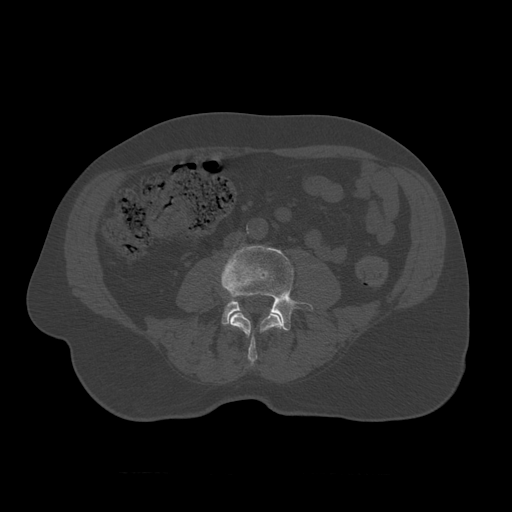
CT including the spine, one axial slice; reconstruction kernel STANDARD; 120 kVp; bone window (W 1800 / L 400 HU); 1.25 mm slice thickness; 512 × 512 image matrix. Patient age 75 years. From the clinical record (not read from this slice): primary cancer: prostate.
Annotated regions visible in this slice (semi-automatic segmentation, software-assisted and operator-edited):
- L3 vertebra: bounding box (x1, y1, x2, y2) in pixels: (230, 311, 284, 367)
- L4 vertebra: (221, 246, 314, 331)